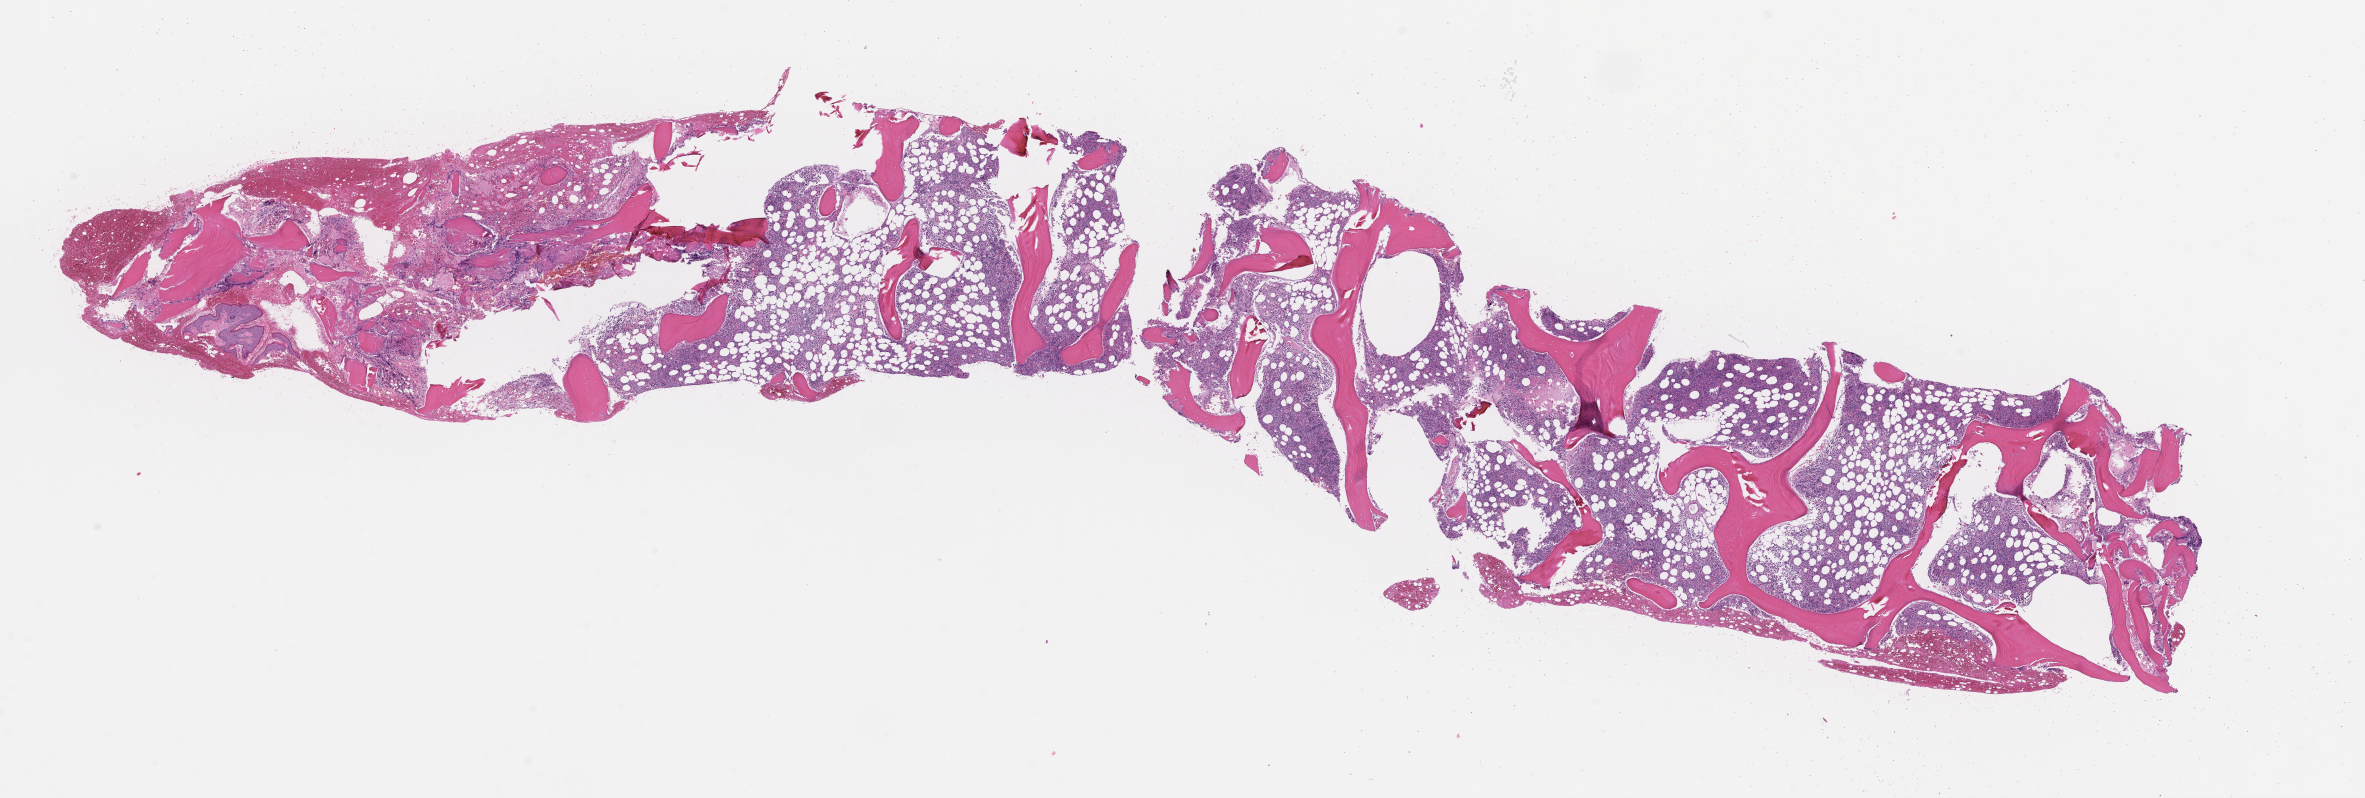
Digitized haematoxylin and eosin-stained section, whole scanned area (about 19.1 x 6.4 mm) shown as a low-resolution overview; formalin-fixed paraffin-embedded section; tissue site: bone marrow; archival tissue. Patient: female.
This section: primary tumour tissue. Diagnosis: Plasma Cell Myeloma.